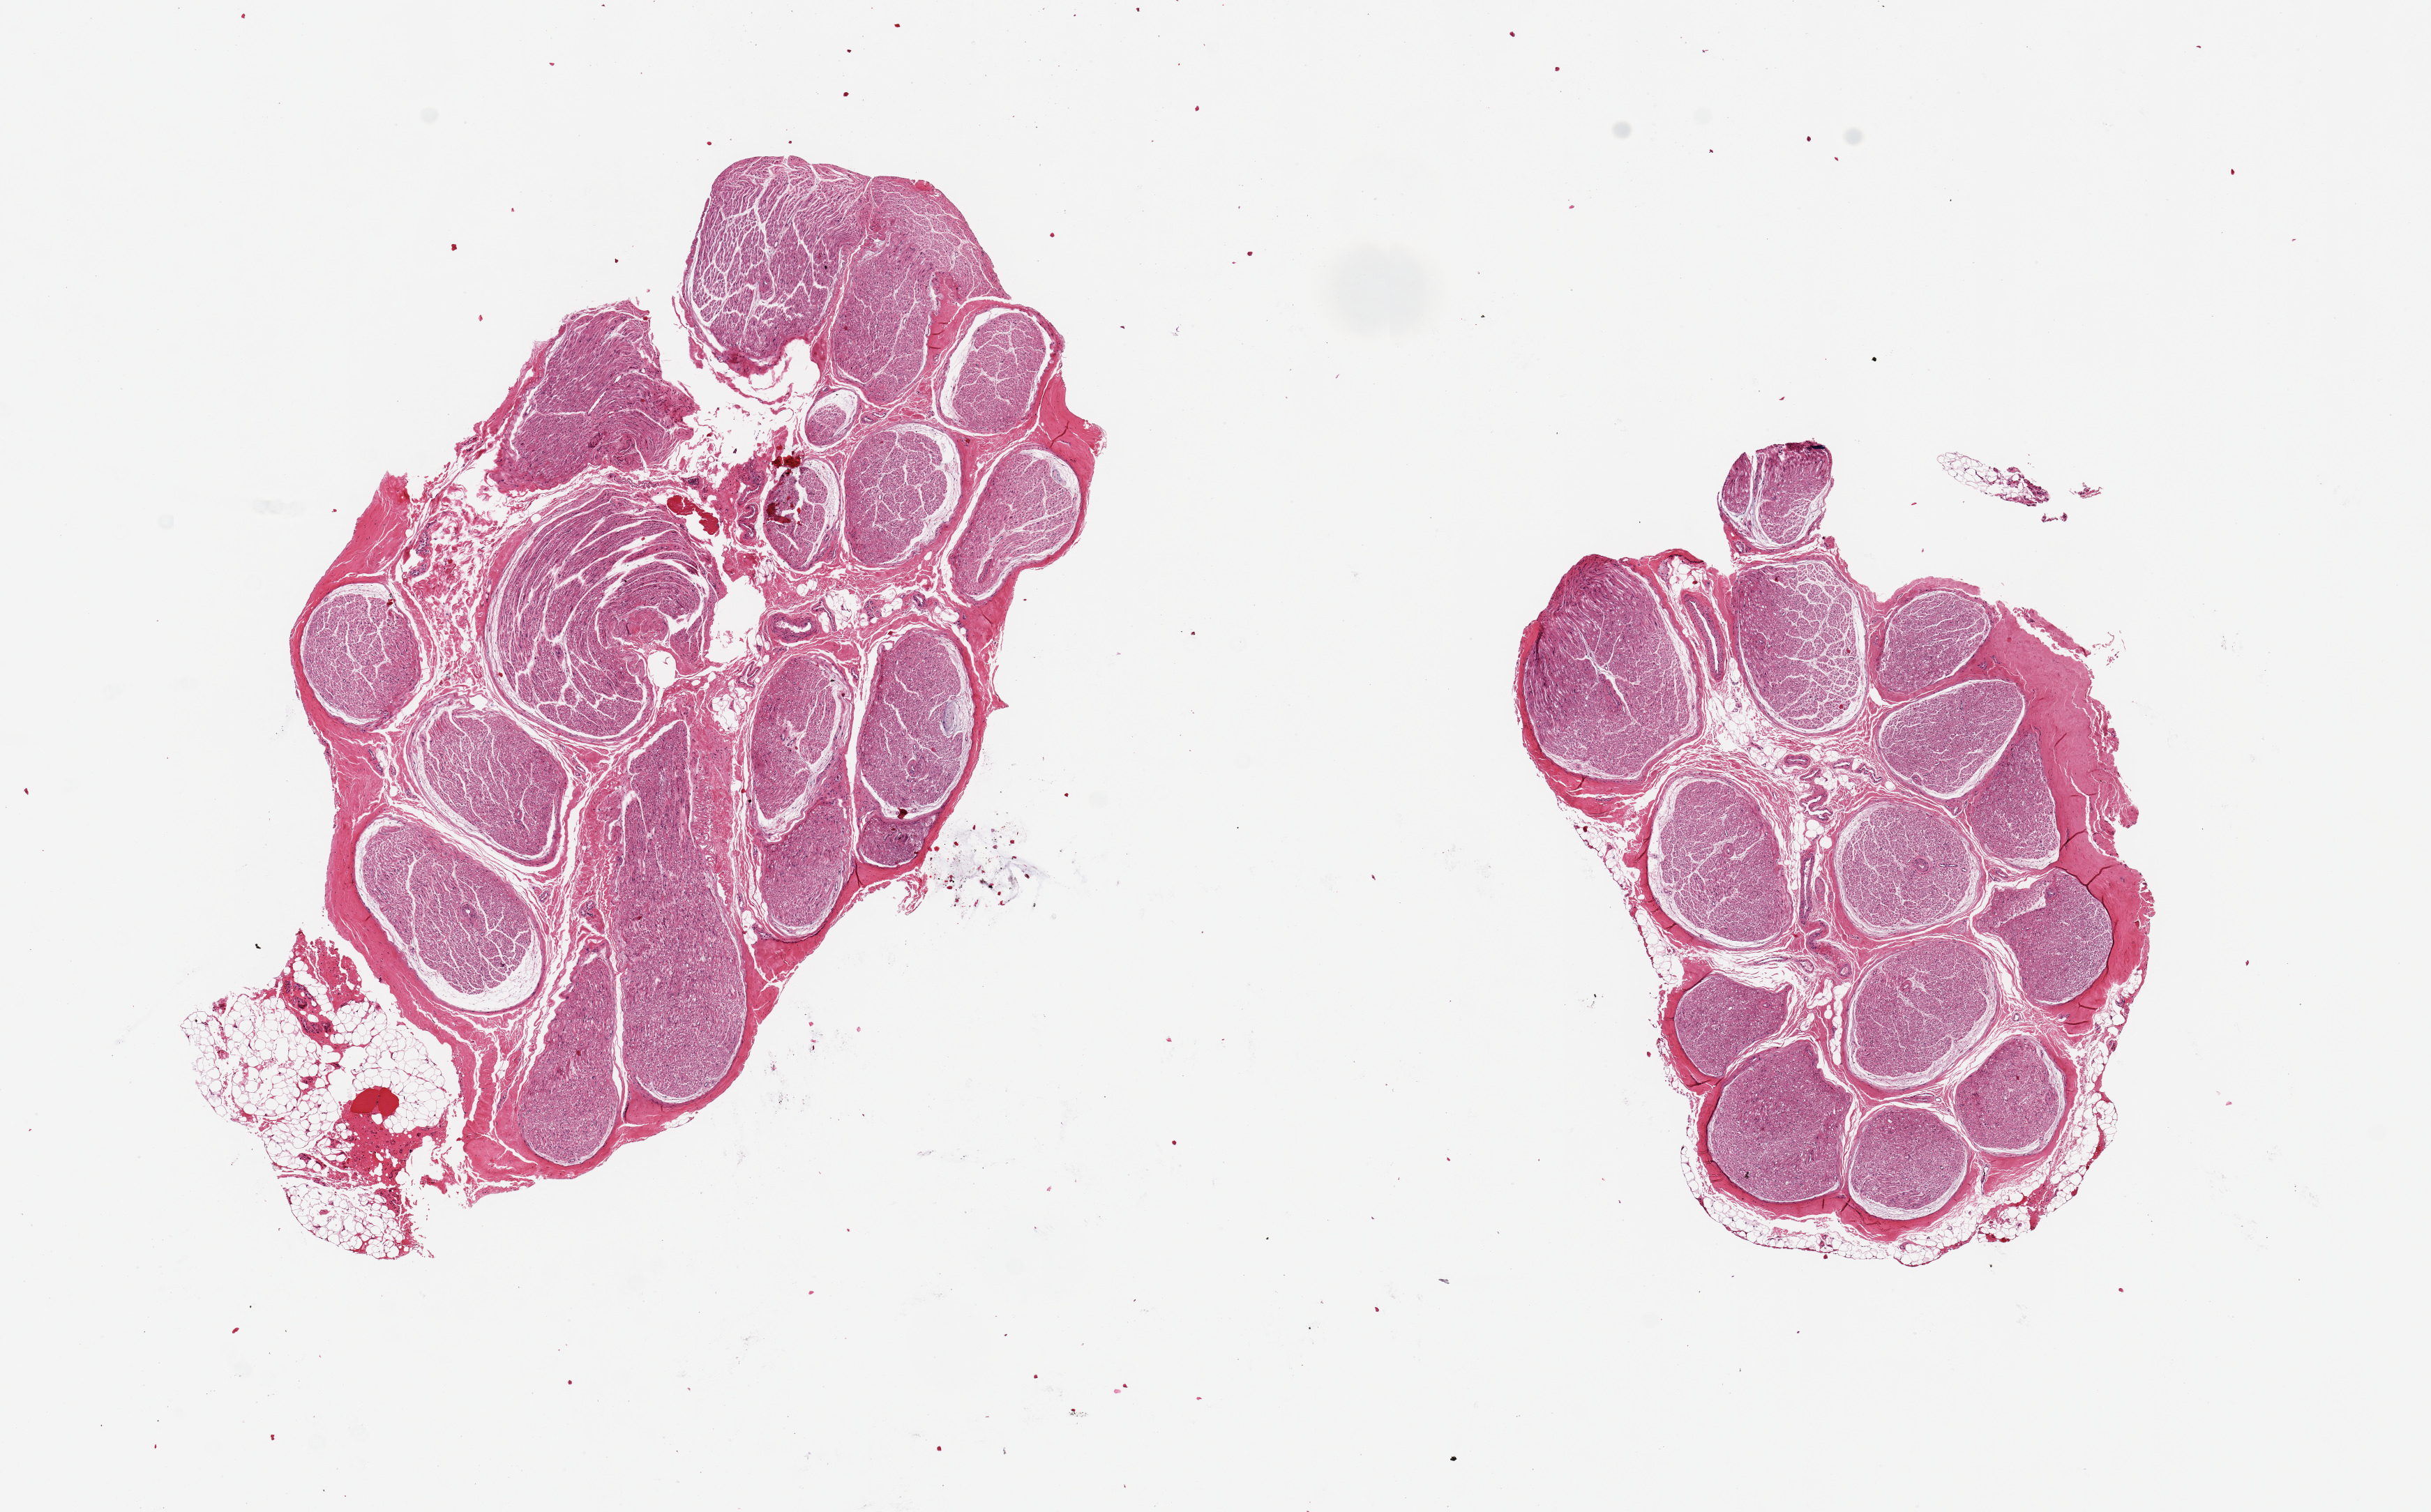
Hematoxylin and eosin (H&E) whole-slide image, shown as a low-resolution overview of the whole scanned area (about 13.8 x 8.6 mm); PAXgene-fixed, paraffin-embedded tissue; target tissue: tibial nerve; donor tissue sample.
Review note (as recorded): 2 pieces, 7x4 & 5x3mm; clean specimens, minimal adherent fat.